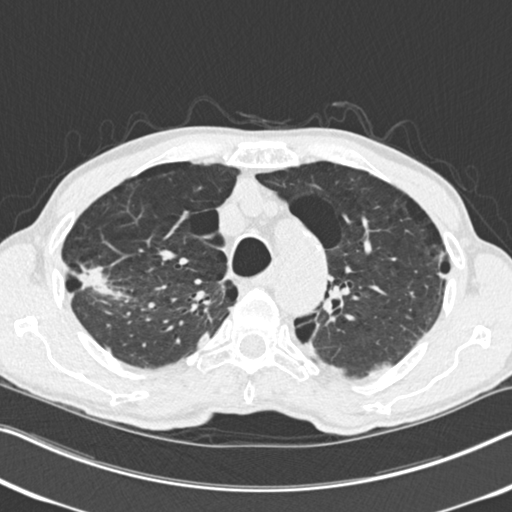
Low-dose screening chest CT, one axial slice. Slice 189 of 251 in the series (ordered by position). 120 kVp. Lung window (W 1500 / L -600 HU). 2 mm slice thickness. 512 × 512 image matrix.
Outlined on this slice (manually delineated by an expert):
- lesion 1 (tumor, upper lobe of right lung): box from (x=77, y=266) to (x=113, y=295) px